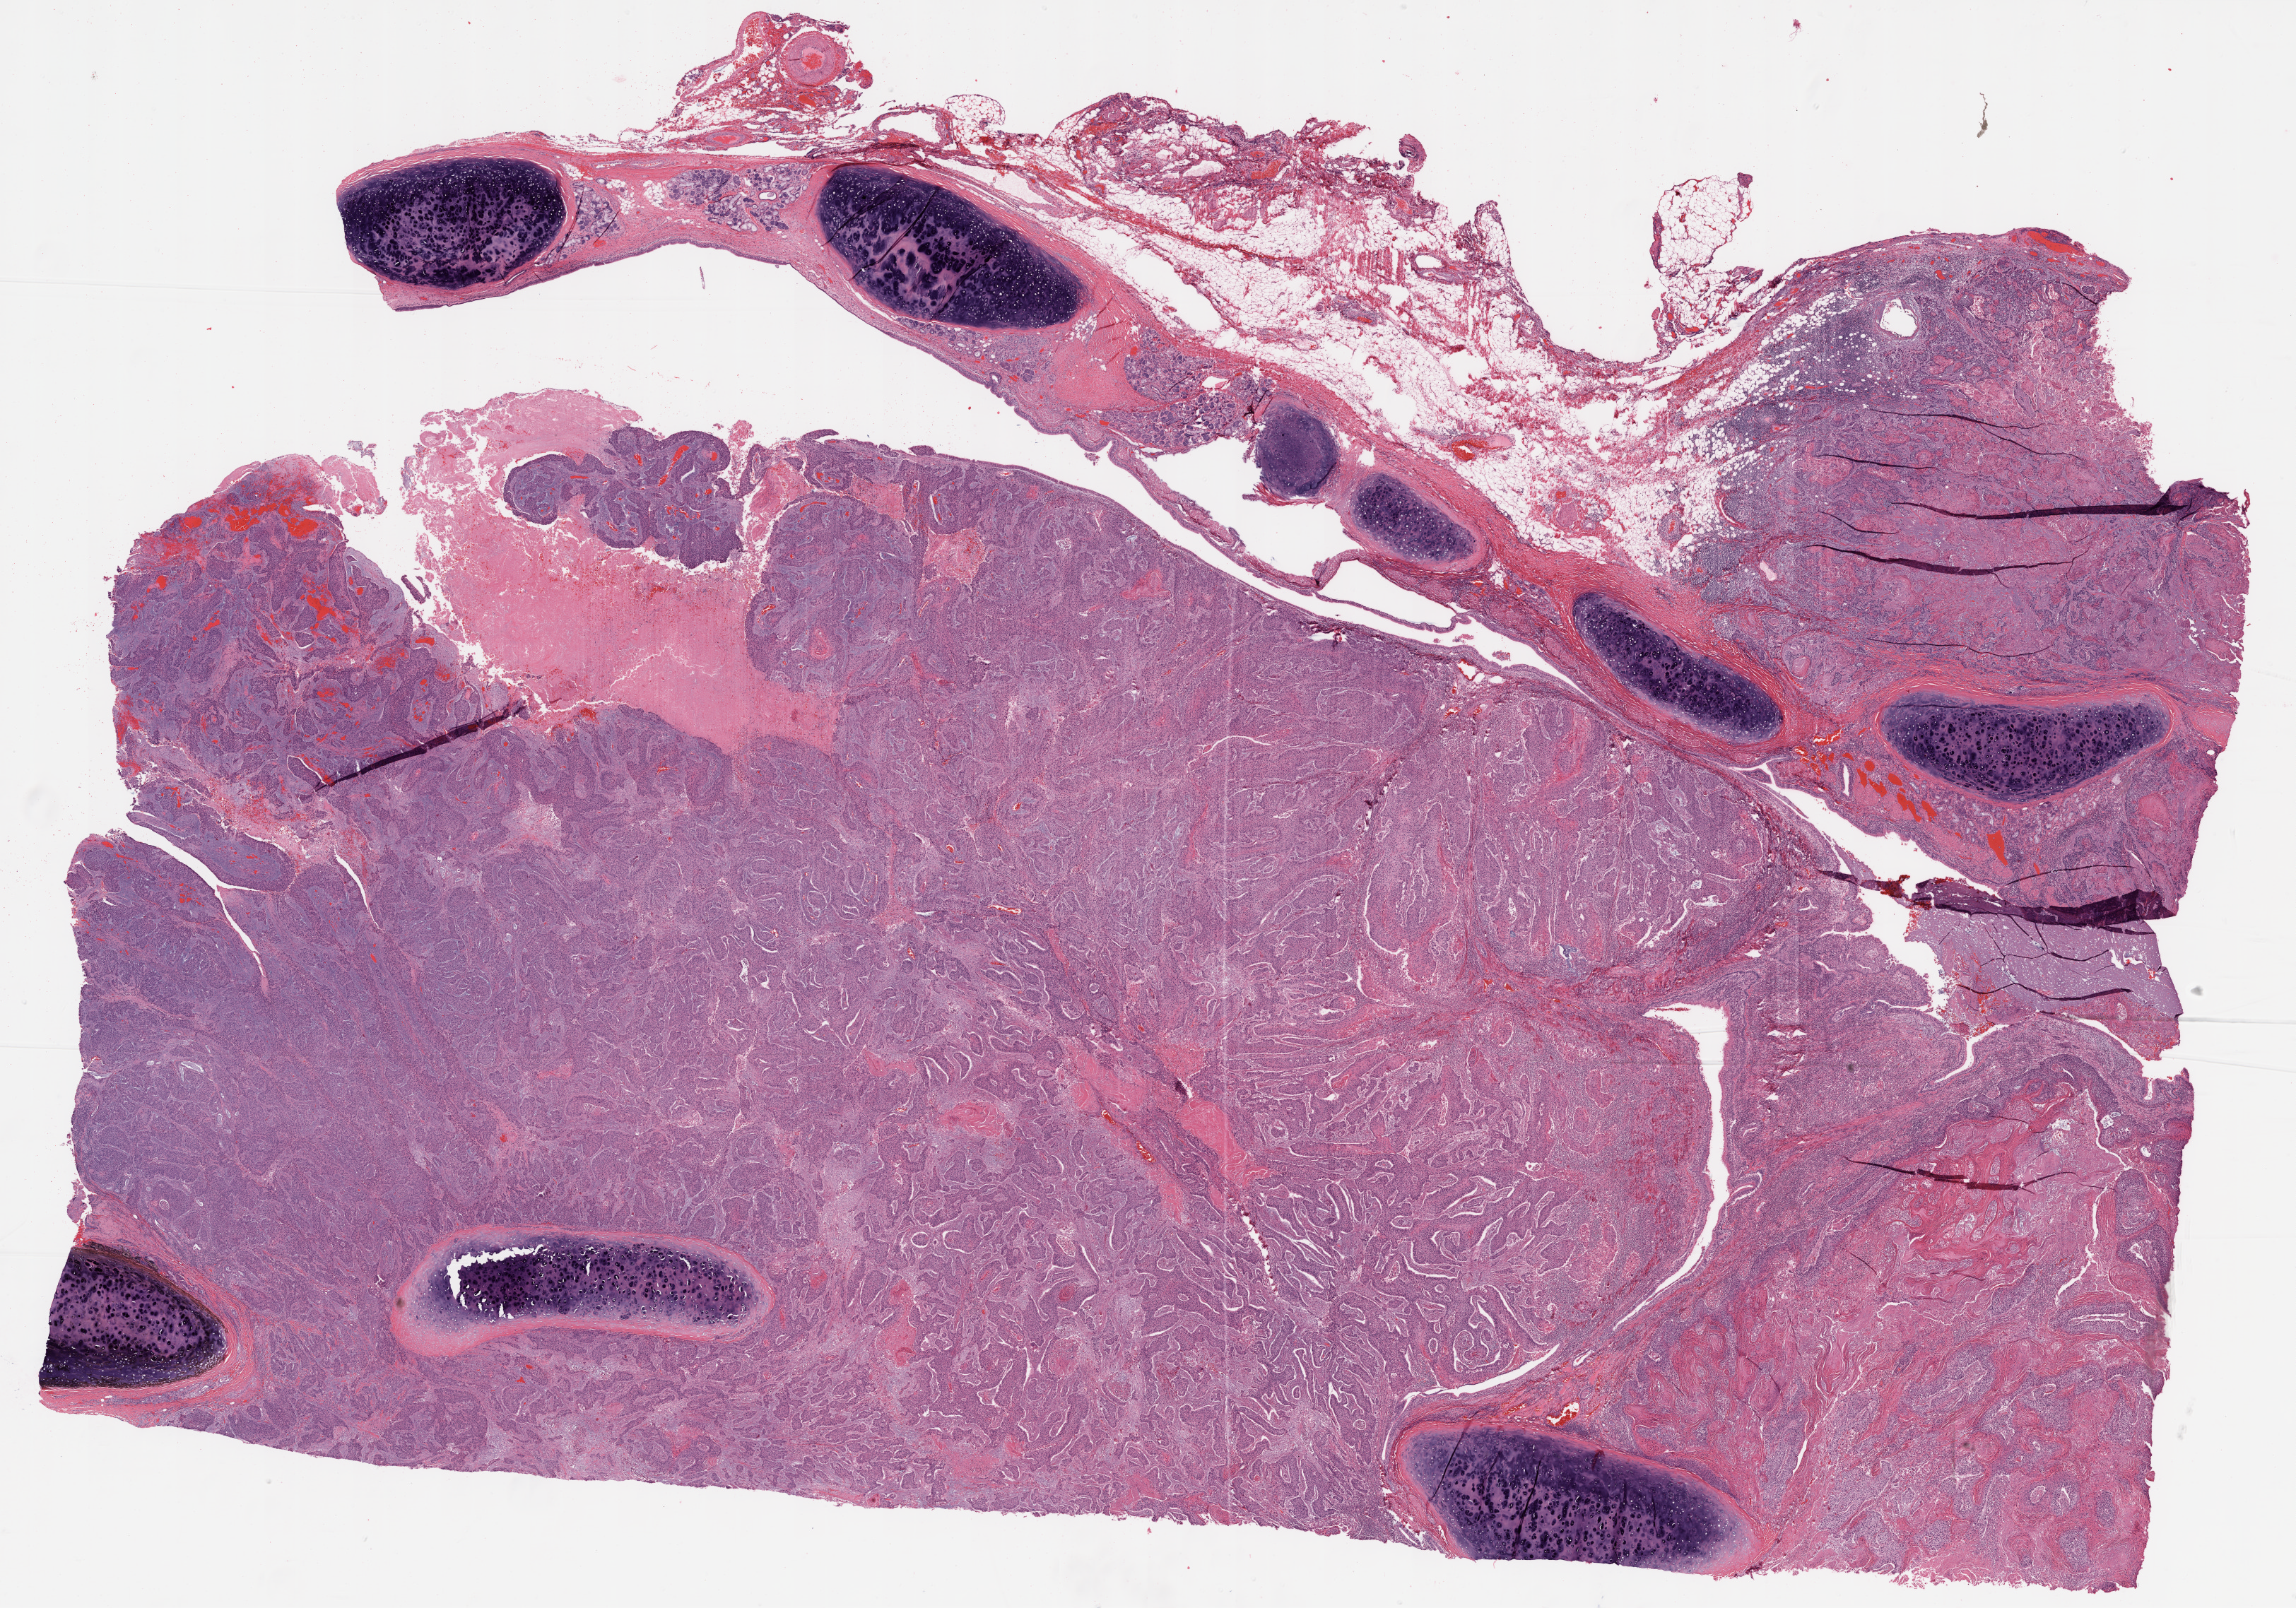
H&E whole-slide image, shown as a low-resolution overview of the whole scanned area (about 26.1 x 18.3 mm); formalin-fixed paraffin-embedded (FFPE) diagnostic section; primary tumour sample from the lung. Patient: female, age at initial diagnosis 60 years.
Histologic diagnosis: Squamous cell carcinoma, NOS. Laterality: right. AJCC pathologic stage: IB.